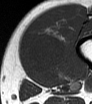
MRI of an extremity soft-tissue mass, one axial slice; slice 15 of 62 in the series (ordered by position); MR volume resampled by the dataset authors to the PET/CT grid (not the native acquisition matrix); 3.27 mm slice thickness; 92 × 104 image matrix. Male patient. From the clinical record (not read from this slice): histological type: mixoid liposarcoma; grade: low; site of the primary tumour: left thigh.
Annotated regions visible in this slice (expert contour drawn on MRI and transferred to this co-registered scan by the dataset authors):
- gross tumour volume (mass): box from (x=25, y=31) to (x=67, y=82) px